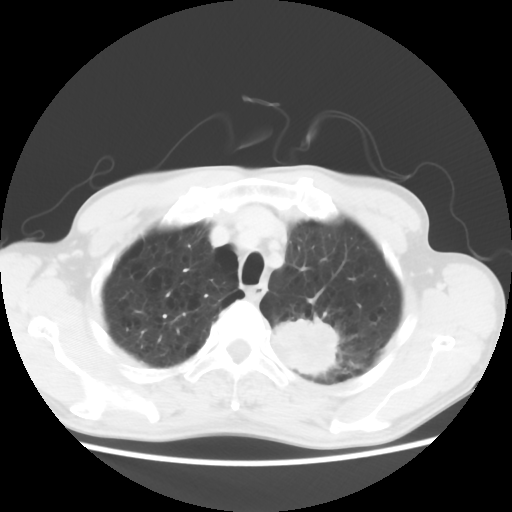
Chest CT, one axial slice. Position 53 of 64 along the scan axis. Lung window (W 1500 / L -600 HU). 5 mm slice thickness. 512 × 512 image matrix, field of view 346 × 346 mm. Male patient, age 63 years. Case-level facts recorded for this patient, not image findings: clinical TNM (as recorded): T2 N0 M0.
Outlined on this slice (bounding box drawn by a radiologist):
- lung tumour (recorded histology: adenocarcinoma): bounding box [x1, y1, x2, y2] px = [267, 312, 345, 392]